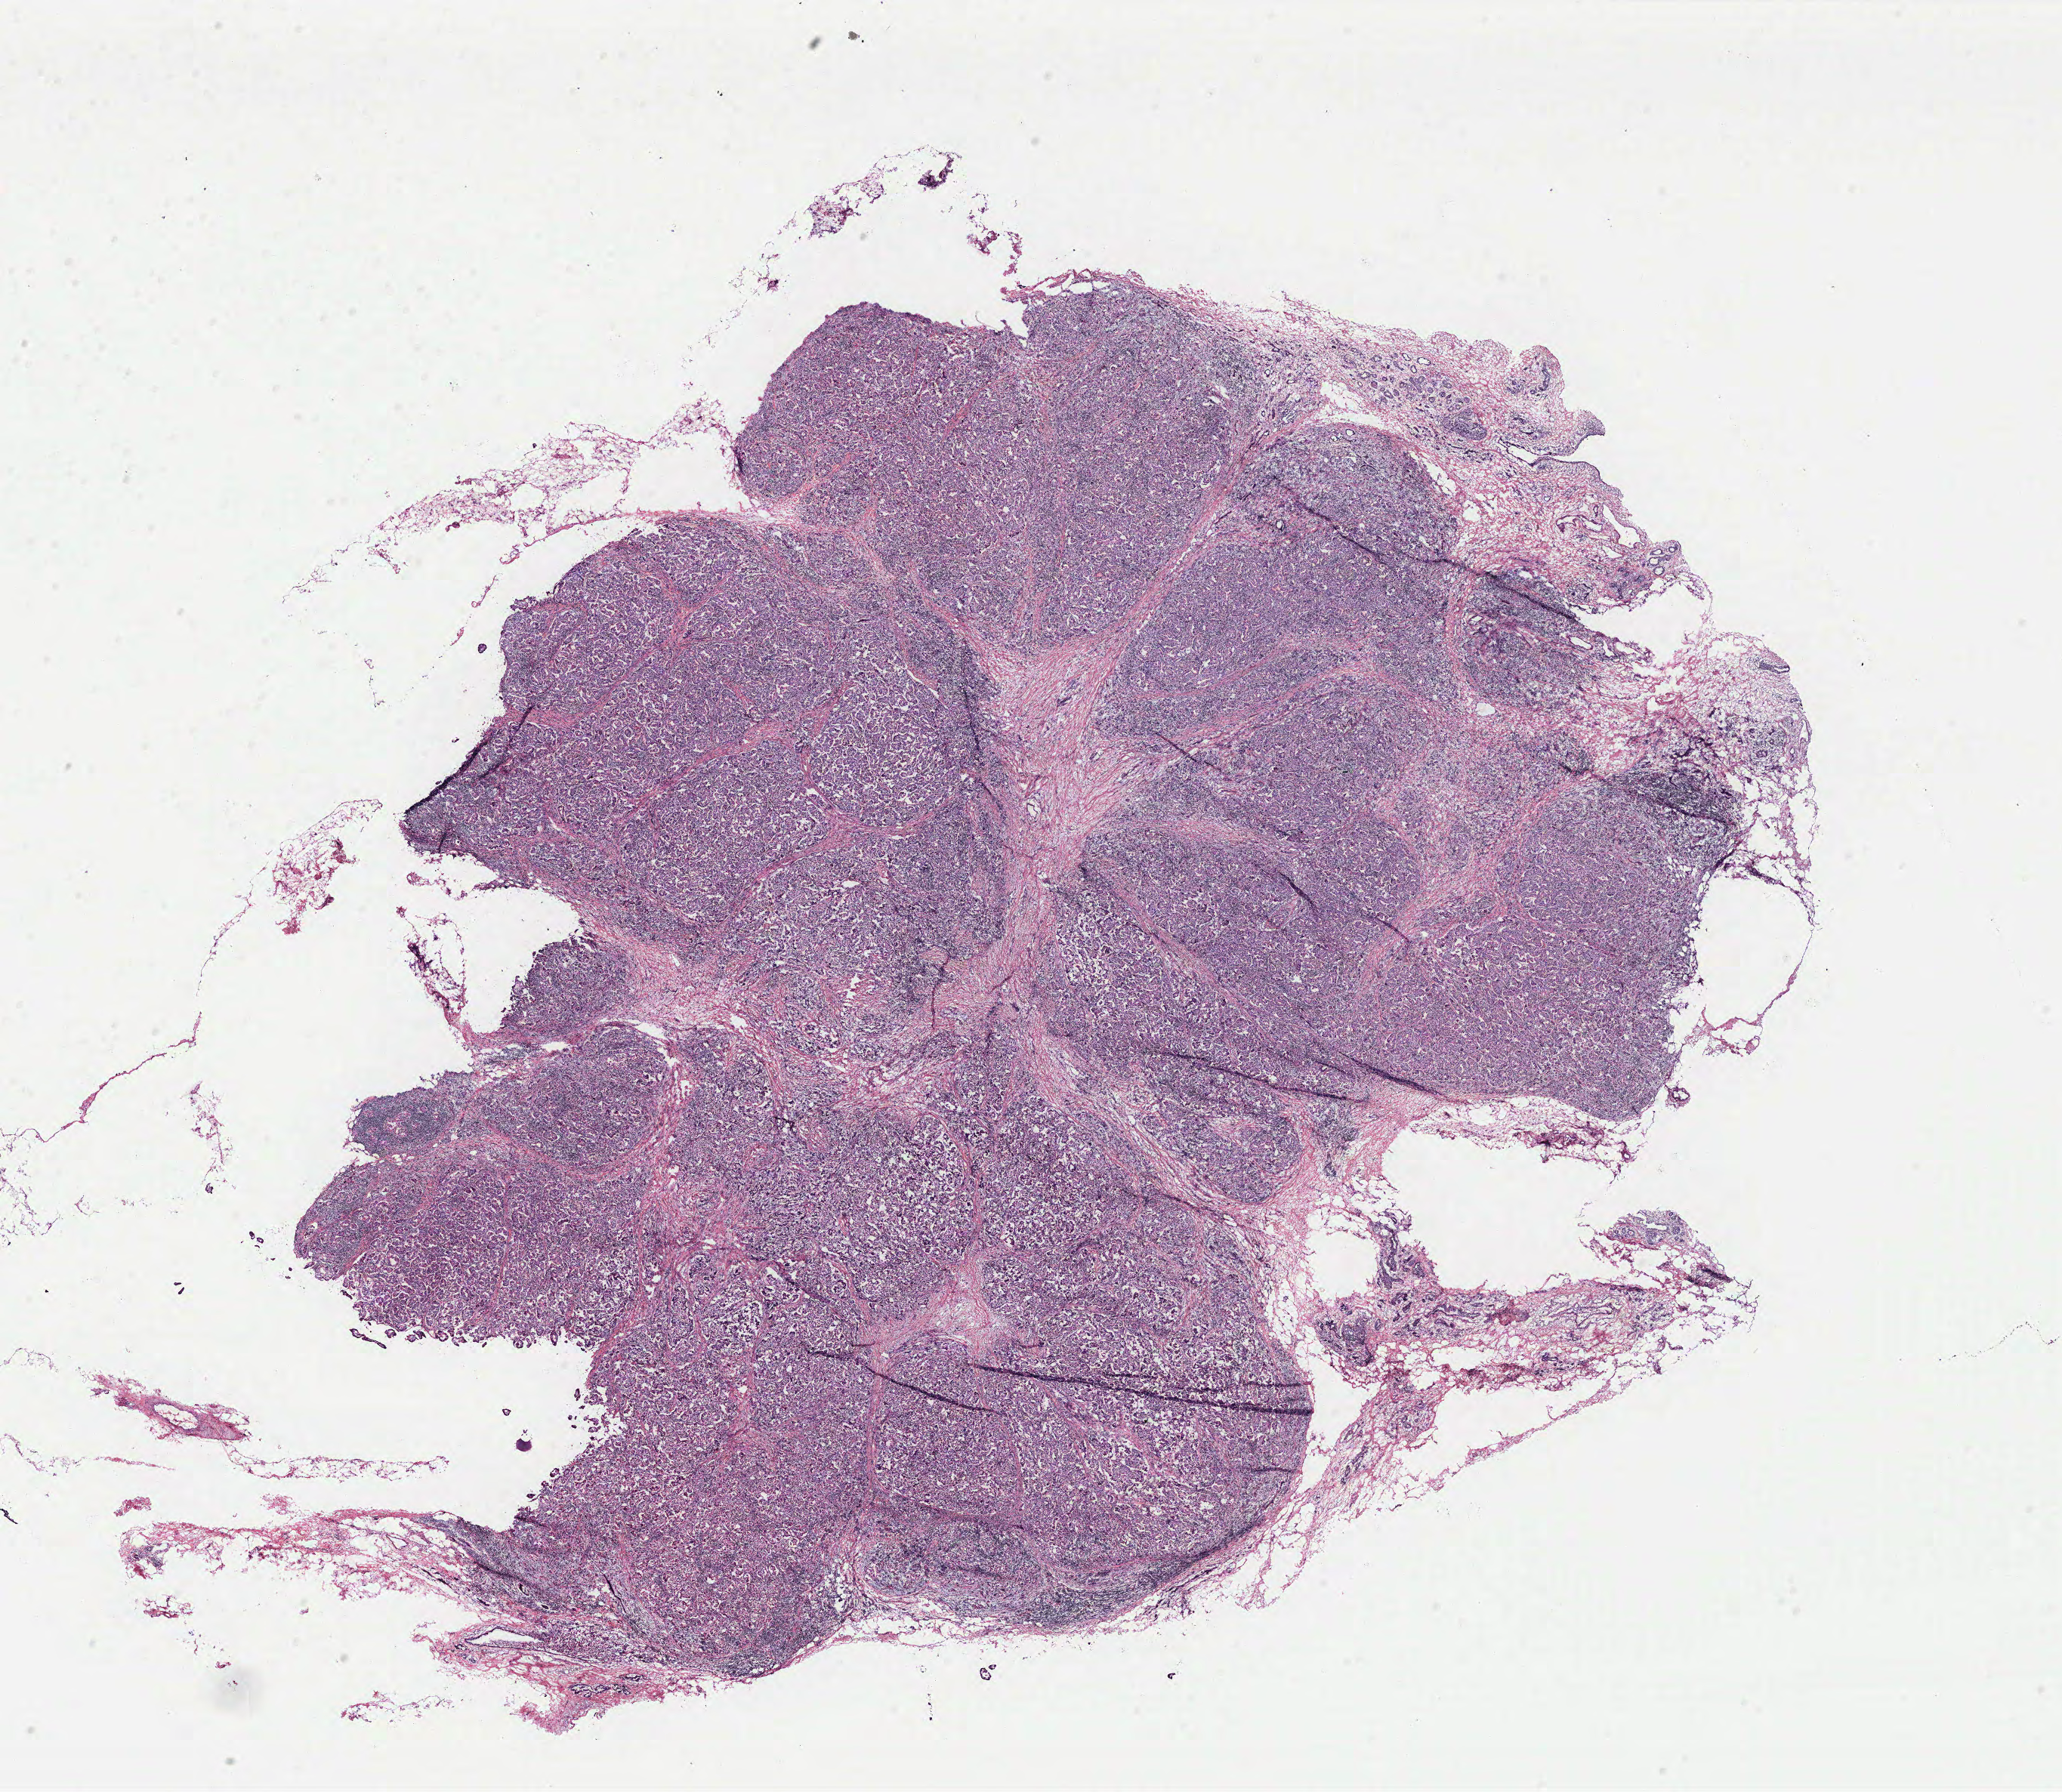
Whole-slide histology image, Hematoxylin and eosin (H&E) stained, shown as a low-resolution overview of the whole scanned area (about 21.8 x 19.0 mm, slide scanned at 40x), breast, tissue type not recorded. Female, 71 y/o.
- patient diagnosis: Infiltrating duct carcinoma, NOS